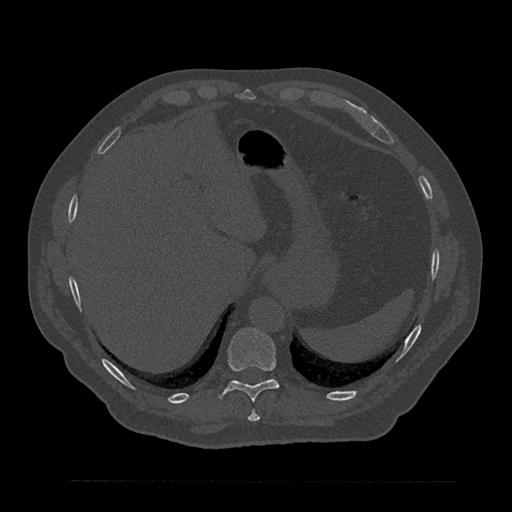
CT including the spine, one axial slice; slice 343 of 797 in the series (ordered by position); bone window (W 1800 / L 400 HU); 512 × 512 image matrix, field of view 430 × 430 mm. Male patient, age 61 years. Case-level facts recorded for this patient, not image findings: primary cancer: prostate.
Outlined on this slice (semi-automatic segmentation, software-assisted and operator-edited):
- T10 vertebra: box from (x=220, y=328) to (x=279, y=402) px
- T9 vertebra: (x=248, y=411)–(x=260, y=422)